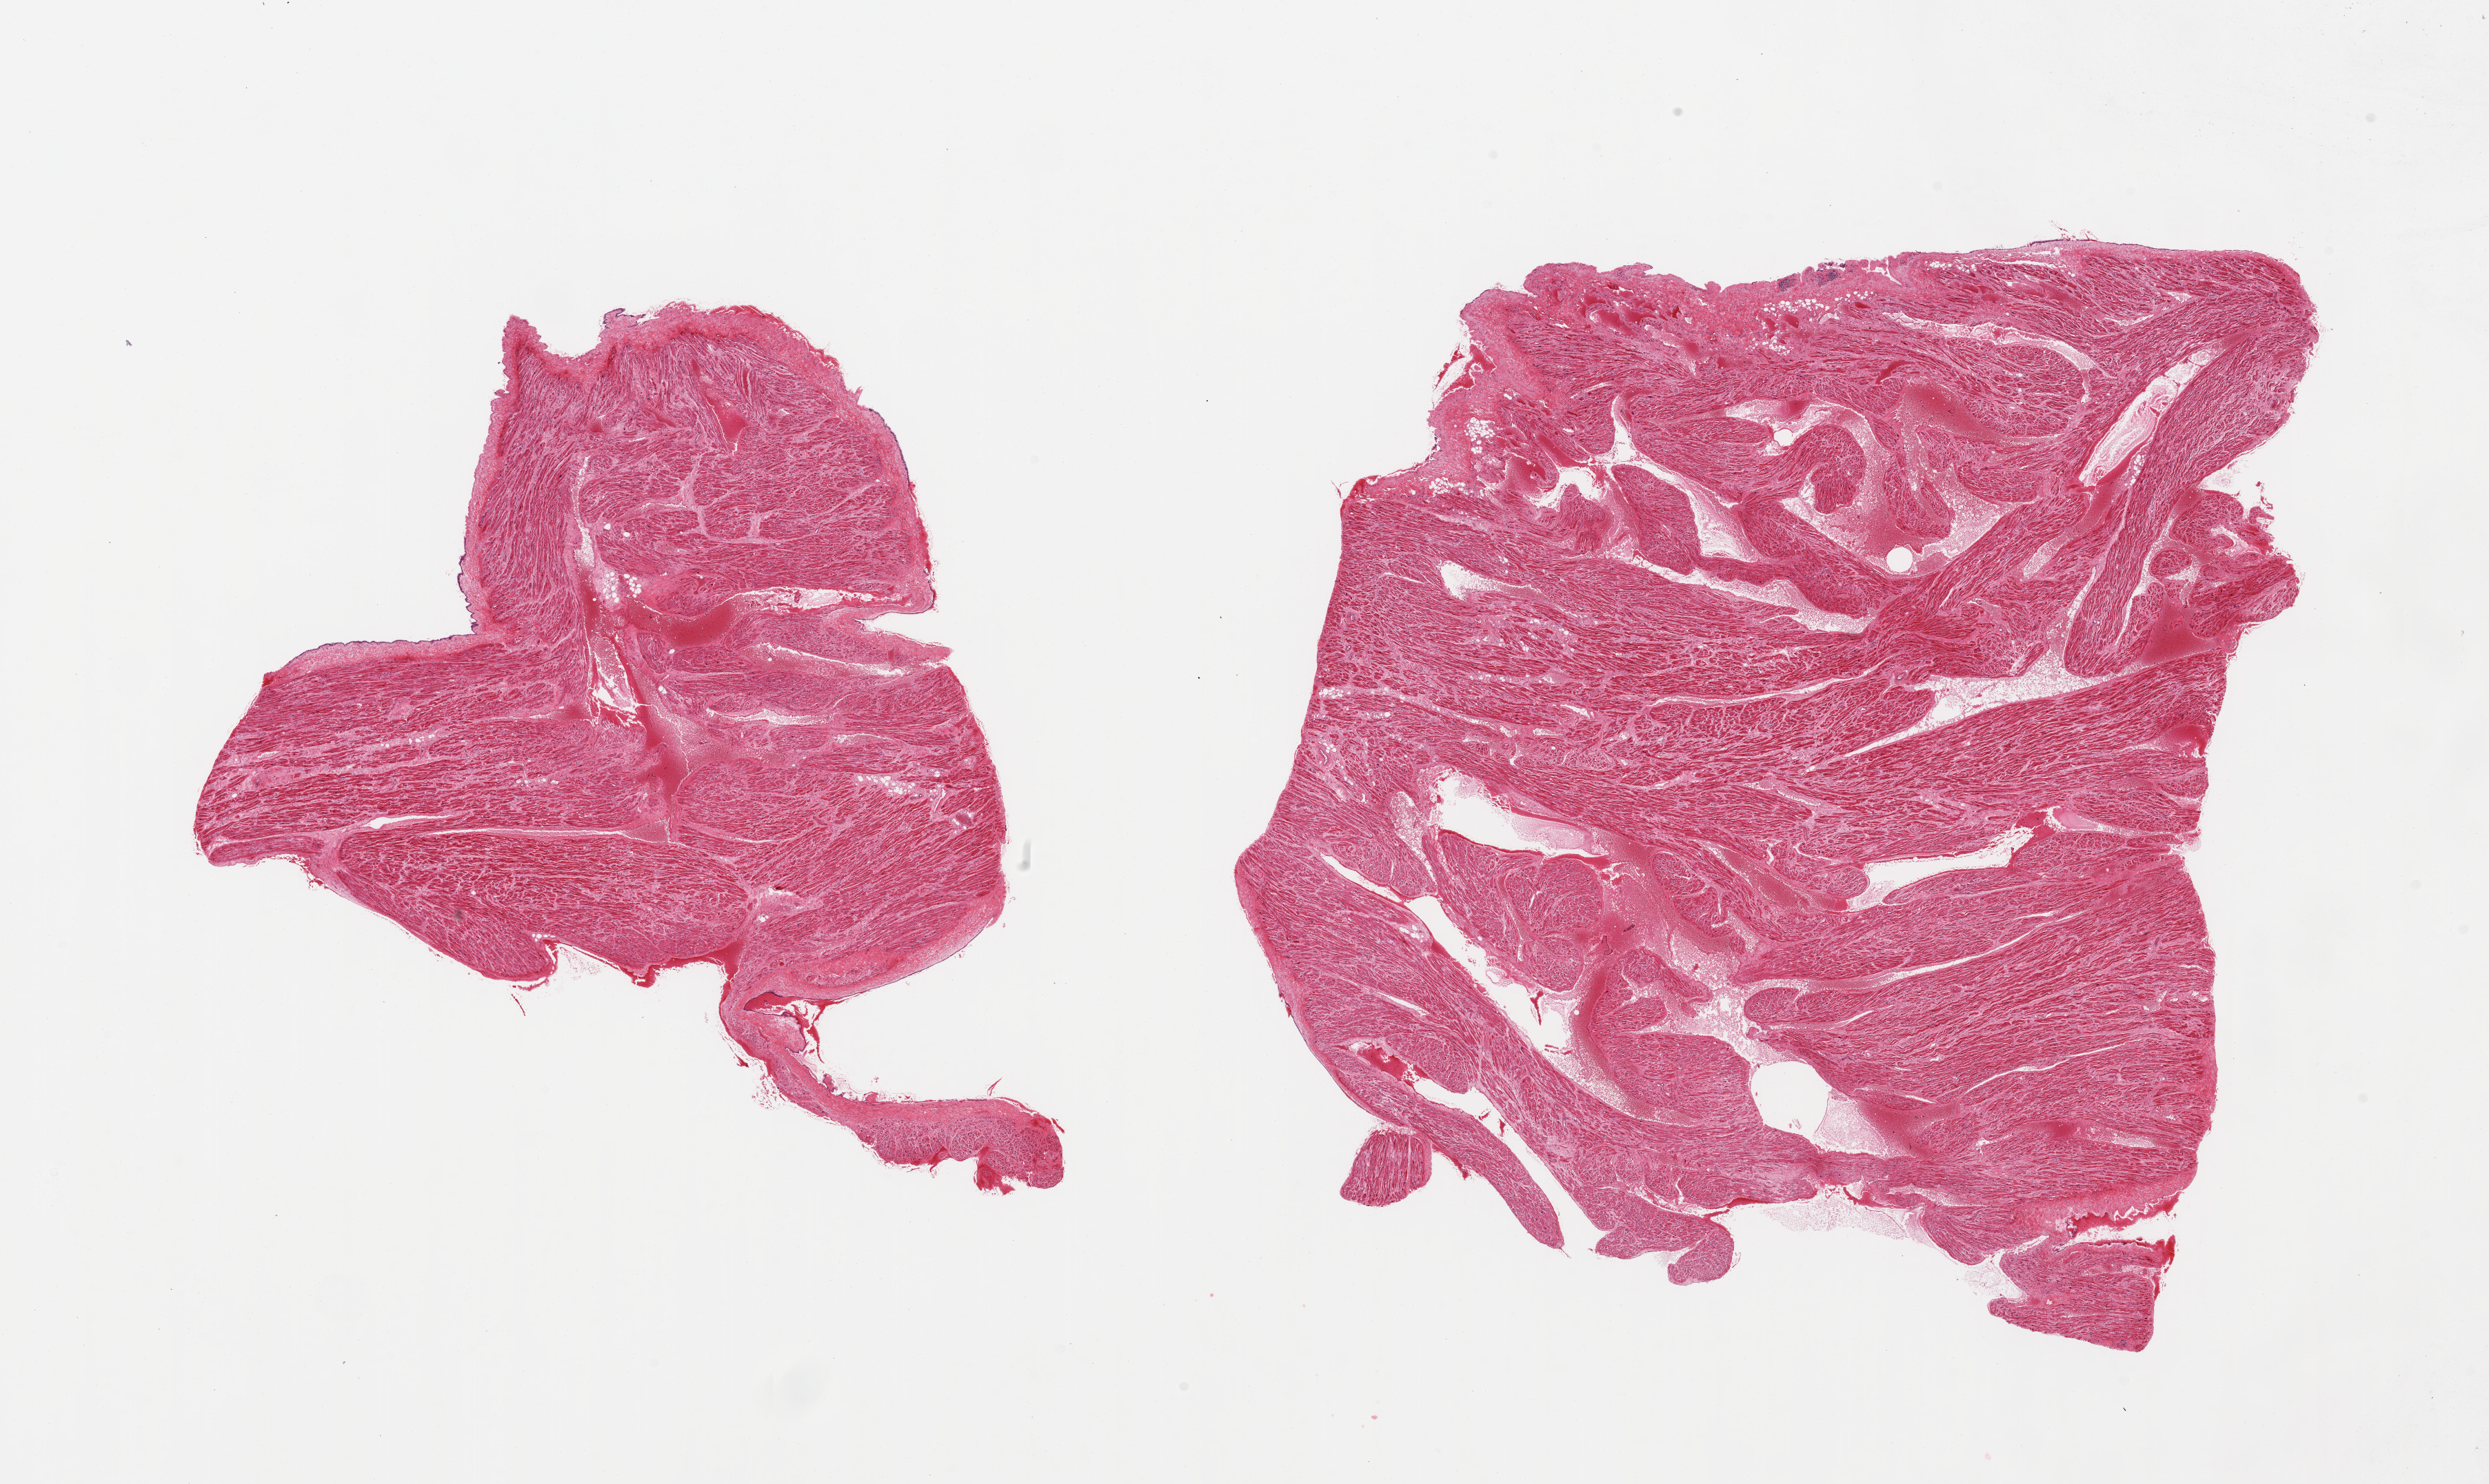
Haematoxylin and eosin whole-slide image, whole scanned area (about 28.5 x 17.0 mm) shown as a low-resolution overview; PAXgene-fixed paraffin-embedded (PFPE) section; target tissue: auricular appendage; donor tissue sample. Male donor.
- pathologist's review note for this sample: 2 pieces; hypertrophy and interstitial fibrosis